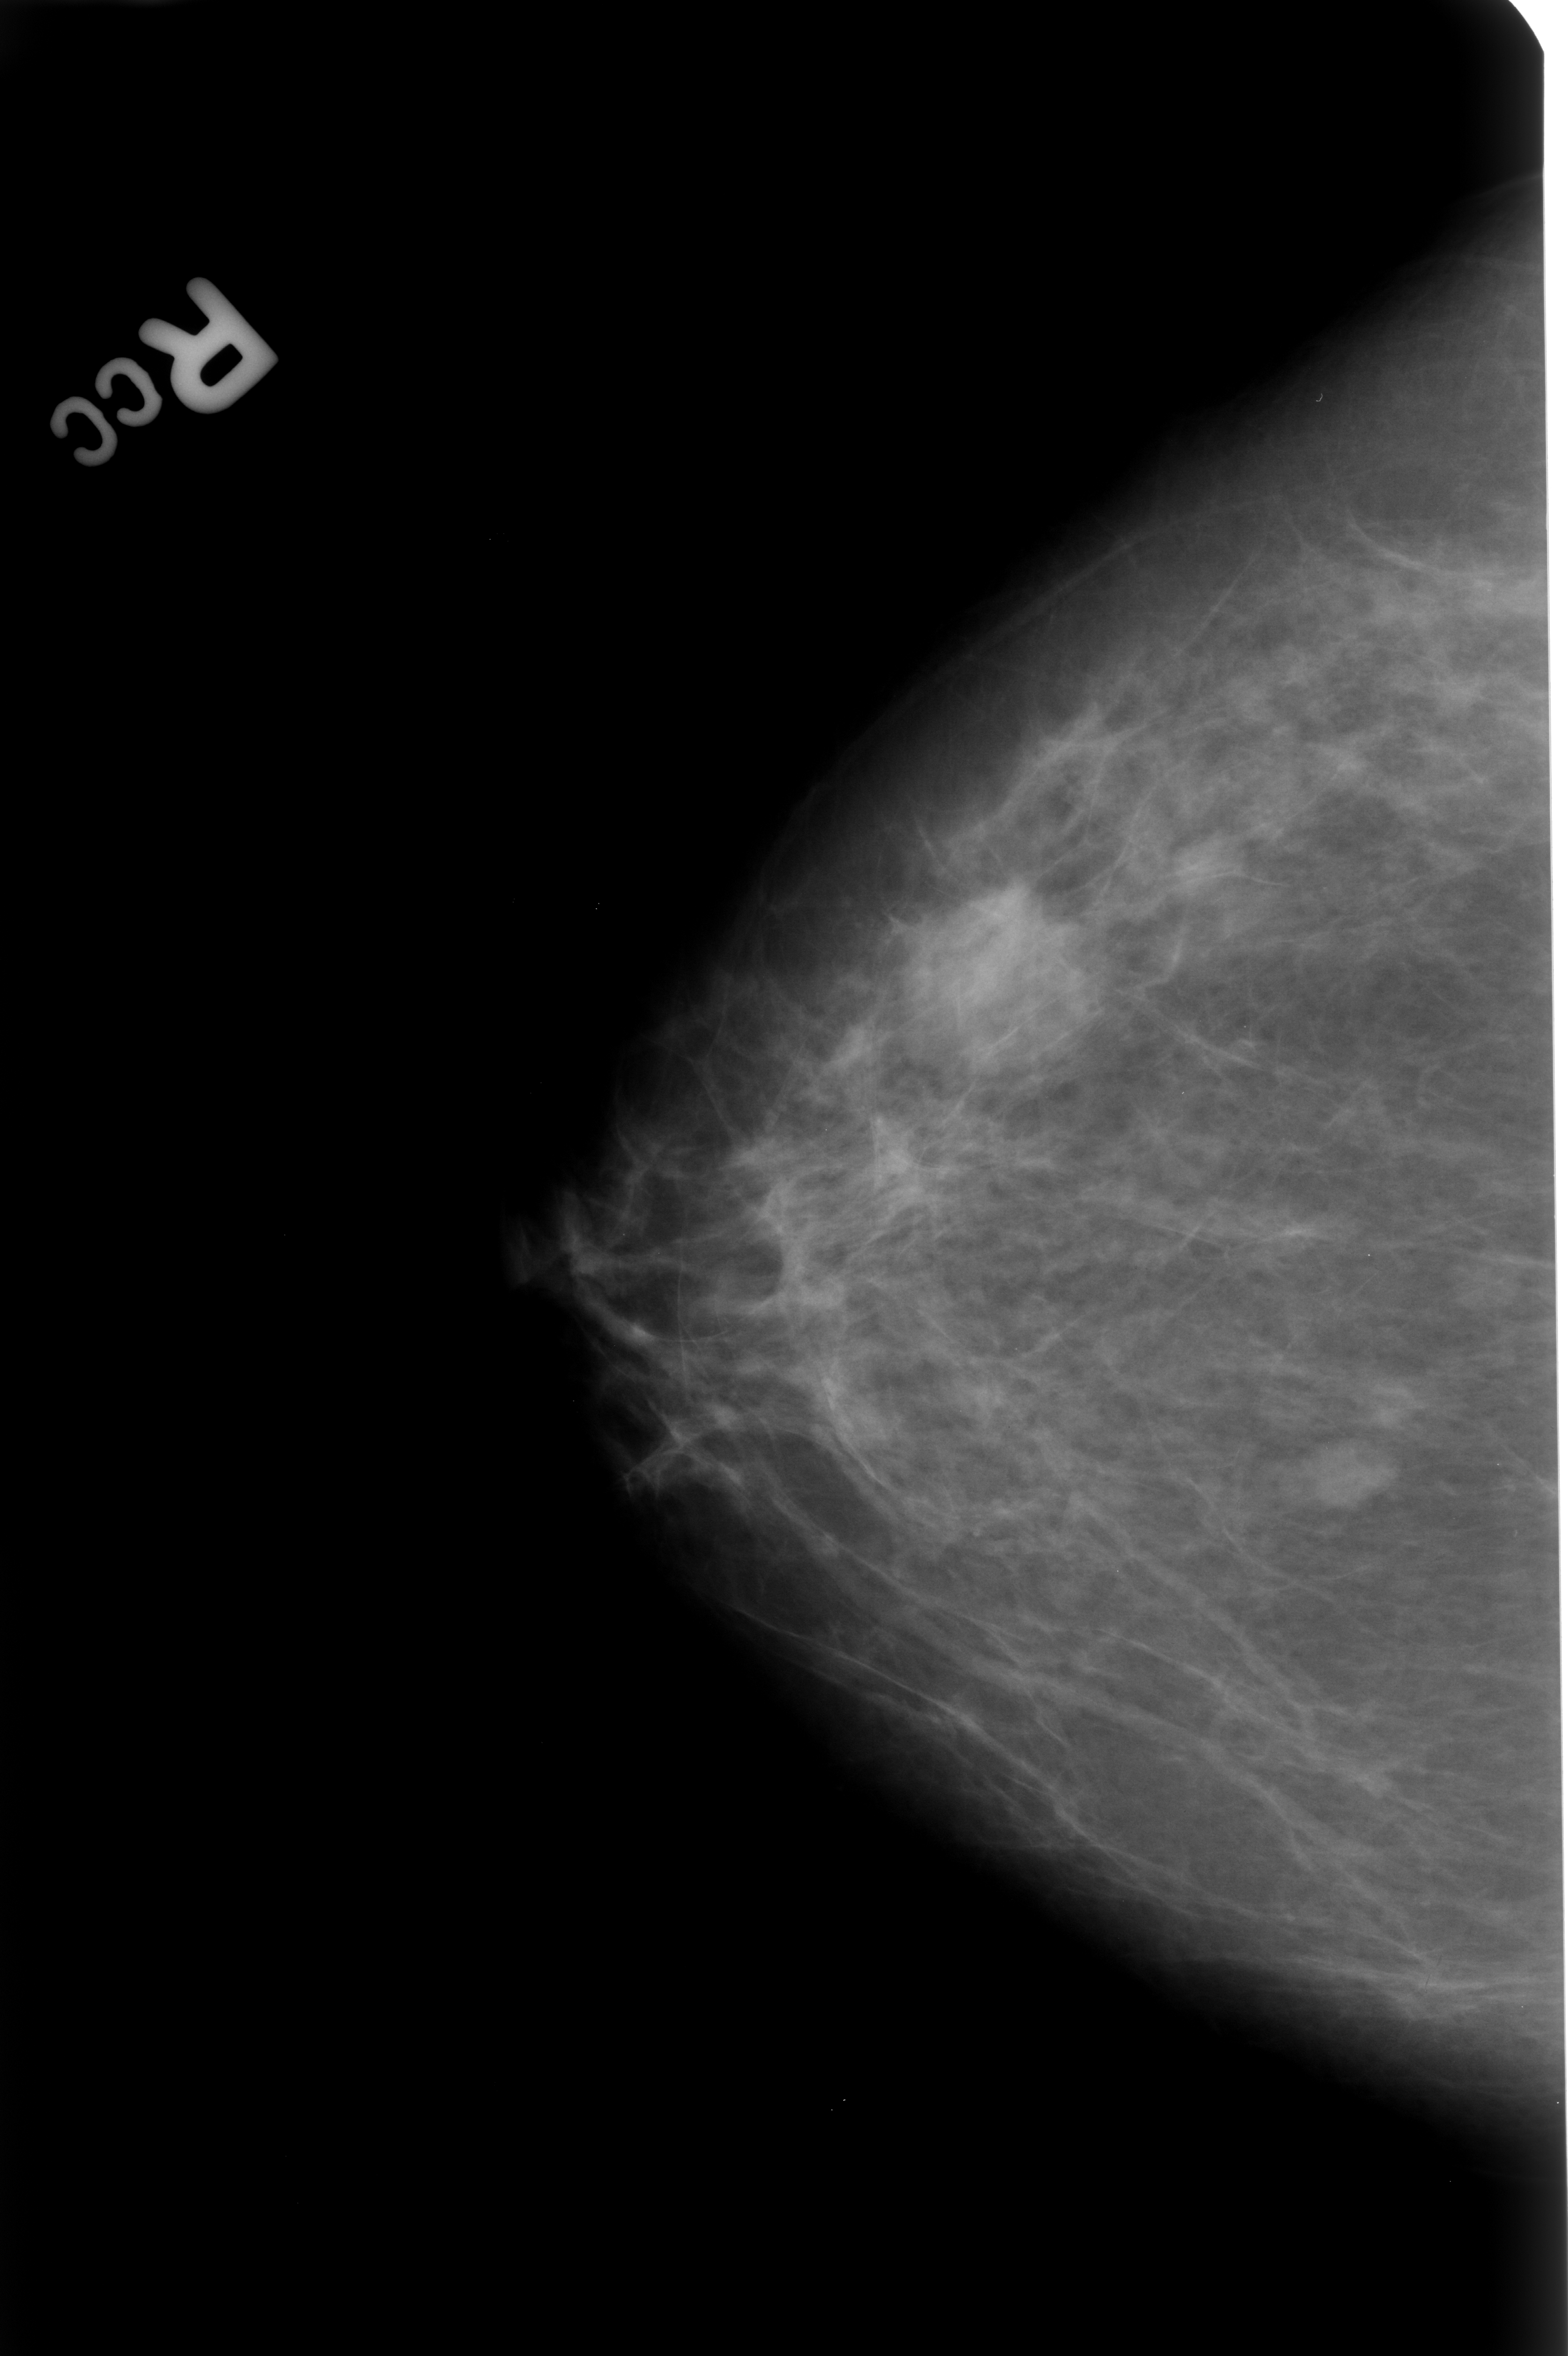
Digitized screen-film mammogram; right breast; craniocaudal (CC) view; breast composition: scattered fibroglandular densities (BI-RADS density category 2 of 4); 1568 × 2356 image matrix.
Expert-marked regions of interest on this image (one box per marked abnormality):
- mass, shape lobulated, margins circumscribed / ill defined; BI-RADS assessment category 4; pathology result (as recorded, not read from the image): benign: bounding box [x1, y1, x2, y2] px = [1278, 1432, 1404, 1514]